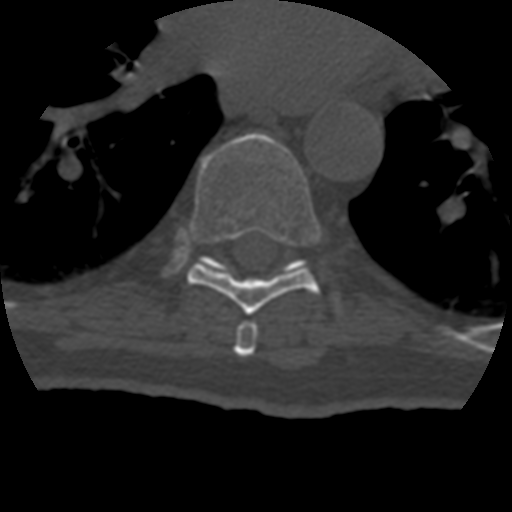
CT including the spine, one axial slice. Position 256 of 399 along the scan axis. 120 kVp. Bone window (W 1800 / L 400 HU). 1.25 mm slice thickness. 512 × 512 image matrix. Patient age 69 years. Case-level facts recorded for this patient, not image findings: primary cancer: prostate.
Annotated regions visible in this slice (semi-automatic segmentation, software-assisted and operator-edited):
- T7 vertebra: box from (x=234, y=321) to (x=258, y=357) px
- T8 vertebra: (x=187, y=133)–(x=319, y=315)
- T9 vertebra: (x=204, y=255)–(x=214, y=264)